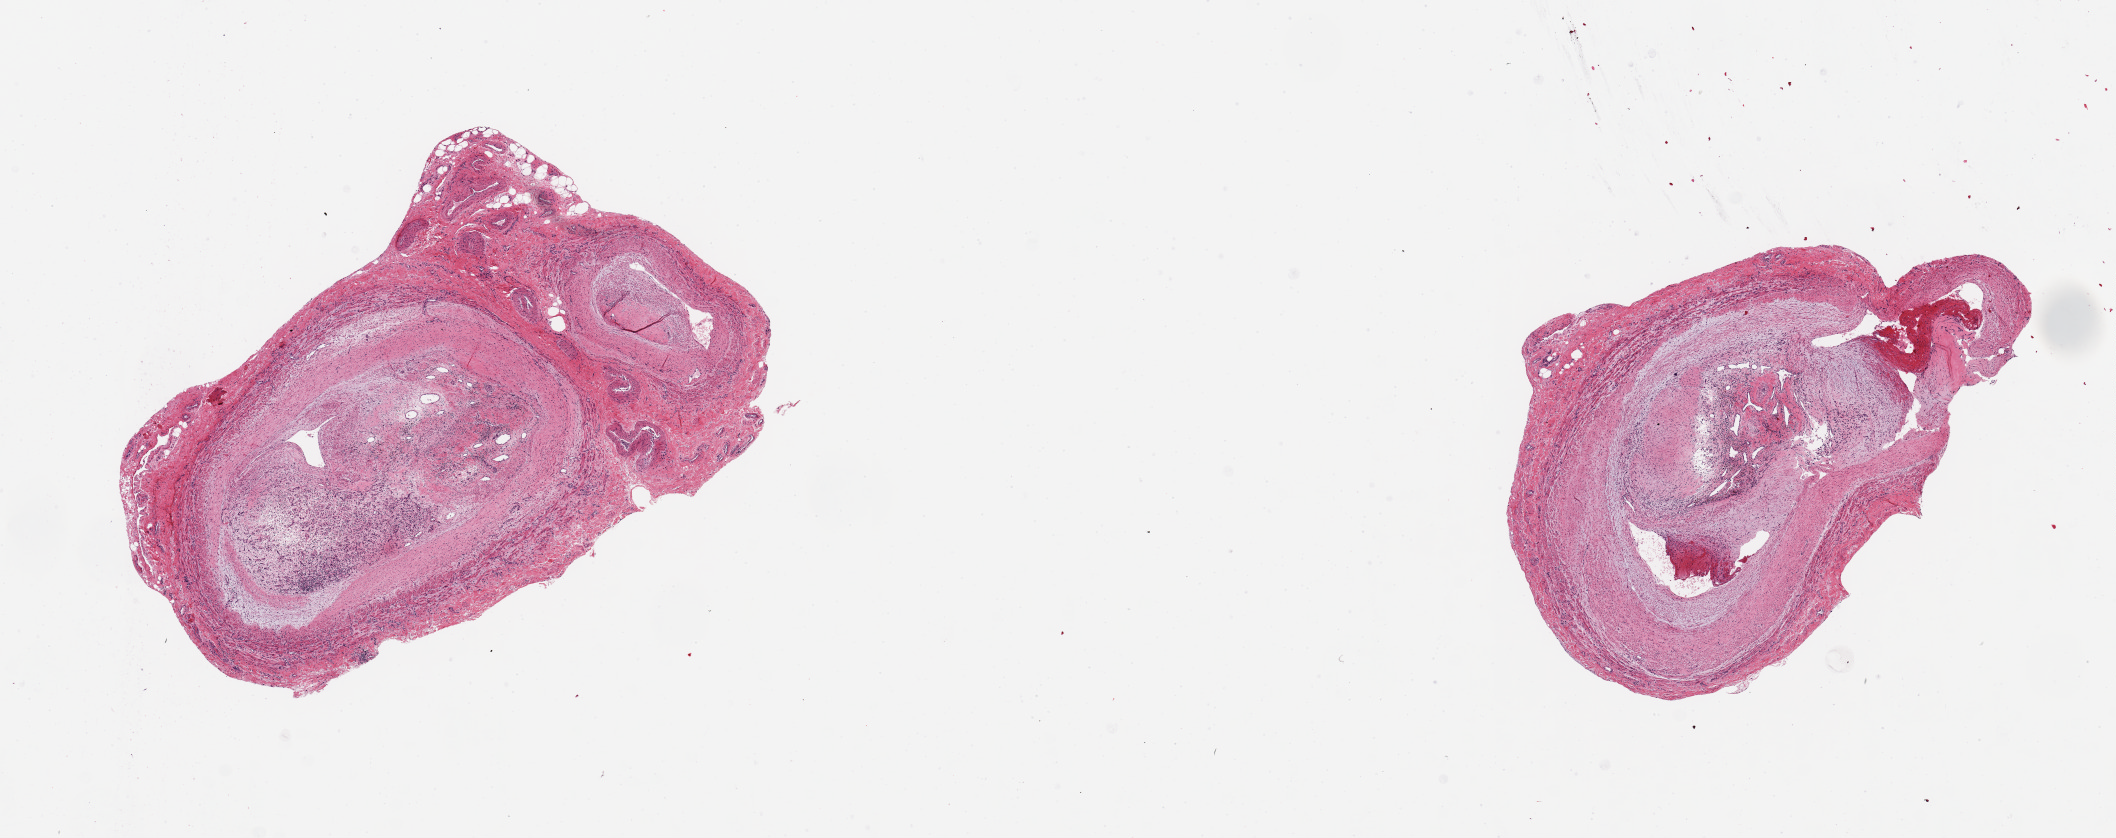
Haematoxylin and eosin whole-slide image, a low-resolution overview of the entire scanned area, about 16.7 x 6.6 mm; PAXgene-fixed paraffin-embedded (PFPE) section; target tissue: tibial artery; tissue donor sample.
Review note (as recorded): 2 pieces ~3mm d; Subtotal occlusive atherosis/thrombosis with recanalization.